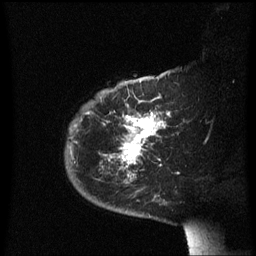
Breast MRI (dynamic contrast-enhanced), one sagittal slice. Dynamic contrast-enhanced series, image 2 of 3 at this slice position (ordered by acquisition). 1.5 T. TE 4.2 ms, TR 8.4 ms. 2.3 mm slice thickness. 256 × 256 image matrix, field of view 200 × 200 mm. Patient: female, 38 years. From the clinical record (not read from this slice): setting: breast cancer imaged before/during neoadjuvant chemotherapy; receptor status: HER2-positive.
Outlined on this slice (semi-automatic segmentation, software-assisted and operator-edited):
- analysis volume of interest (the breast-tissue region the enhancement analysis was run in; not a lesion): box from (x=65, y=78) to (x=172, y=213) px
- tumour enhancement mask (voxels above the 70 % enhancement threshold inside the analysis volume of interest): (x=88, y=112)–(x=169, y=177)